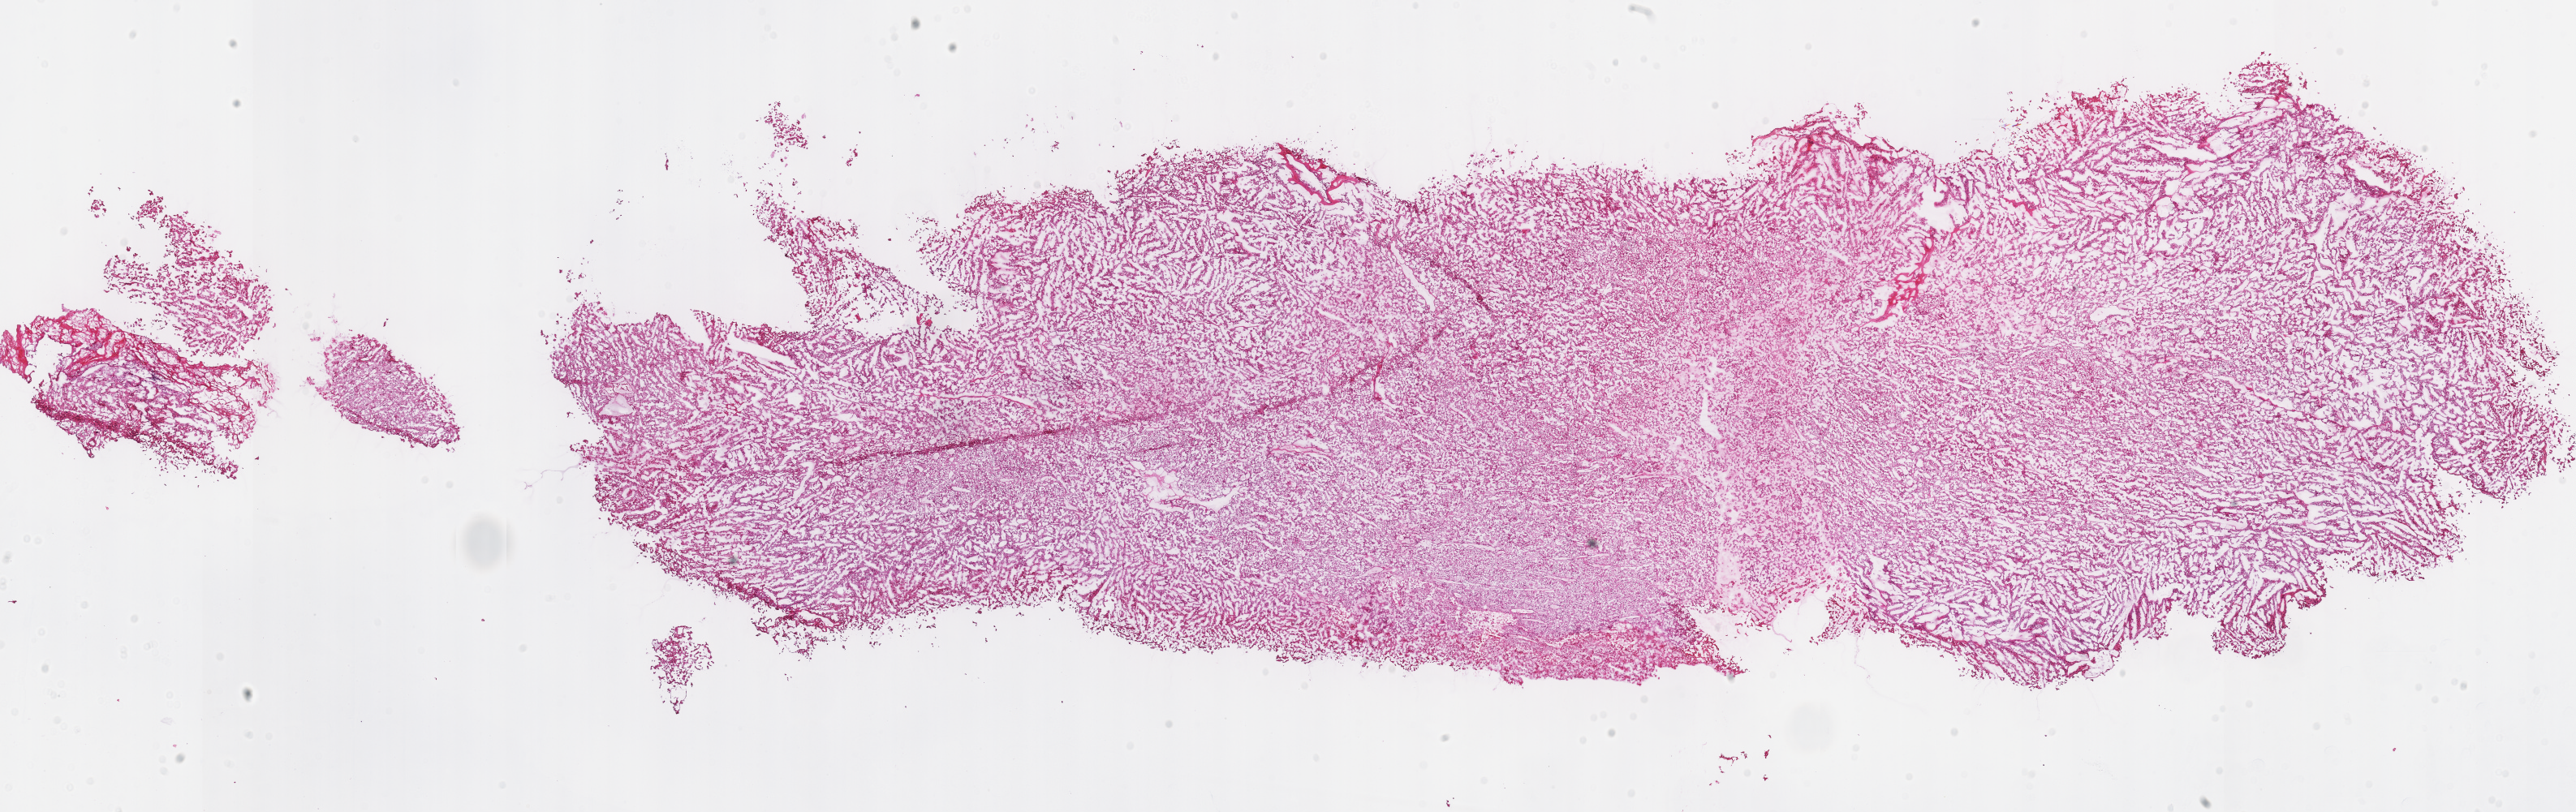
Digitized H&E tissue section (whole slide), shown as a low-resolution overview of the whole scanned area (about 25.0 x 7.9 mm, slide scanned at 40x); frozen section from the top of the tissue portion; sample: primary tumour, kidney. Patient: female, age at initial diagnosis 50 years. Composition of this section per pathologist review: tumour cells 90%, tumour nuclei 90%, normal cells 0%, stromal cells 10%, necrosis 0%.
AJCC pathologic stage: II (7th edition). Pathologic diagnosis: Renal cell carcinoma, chromophobe type.